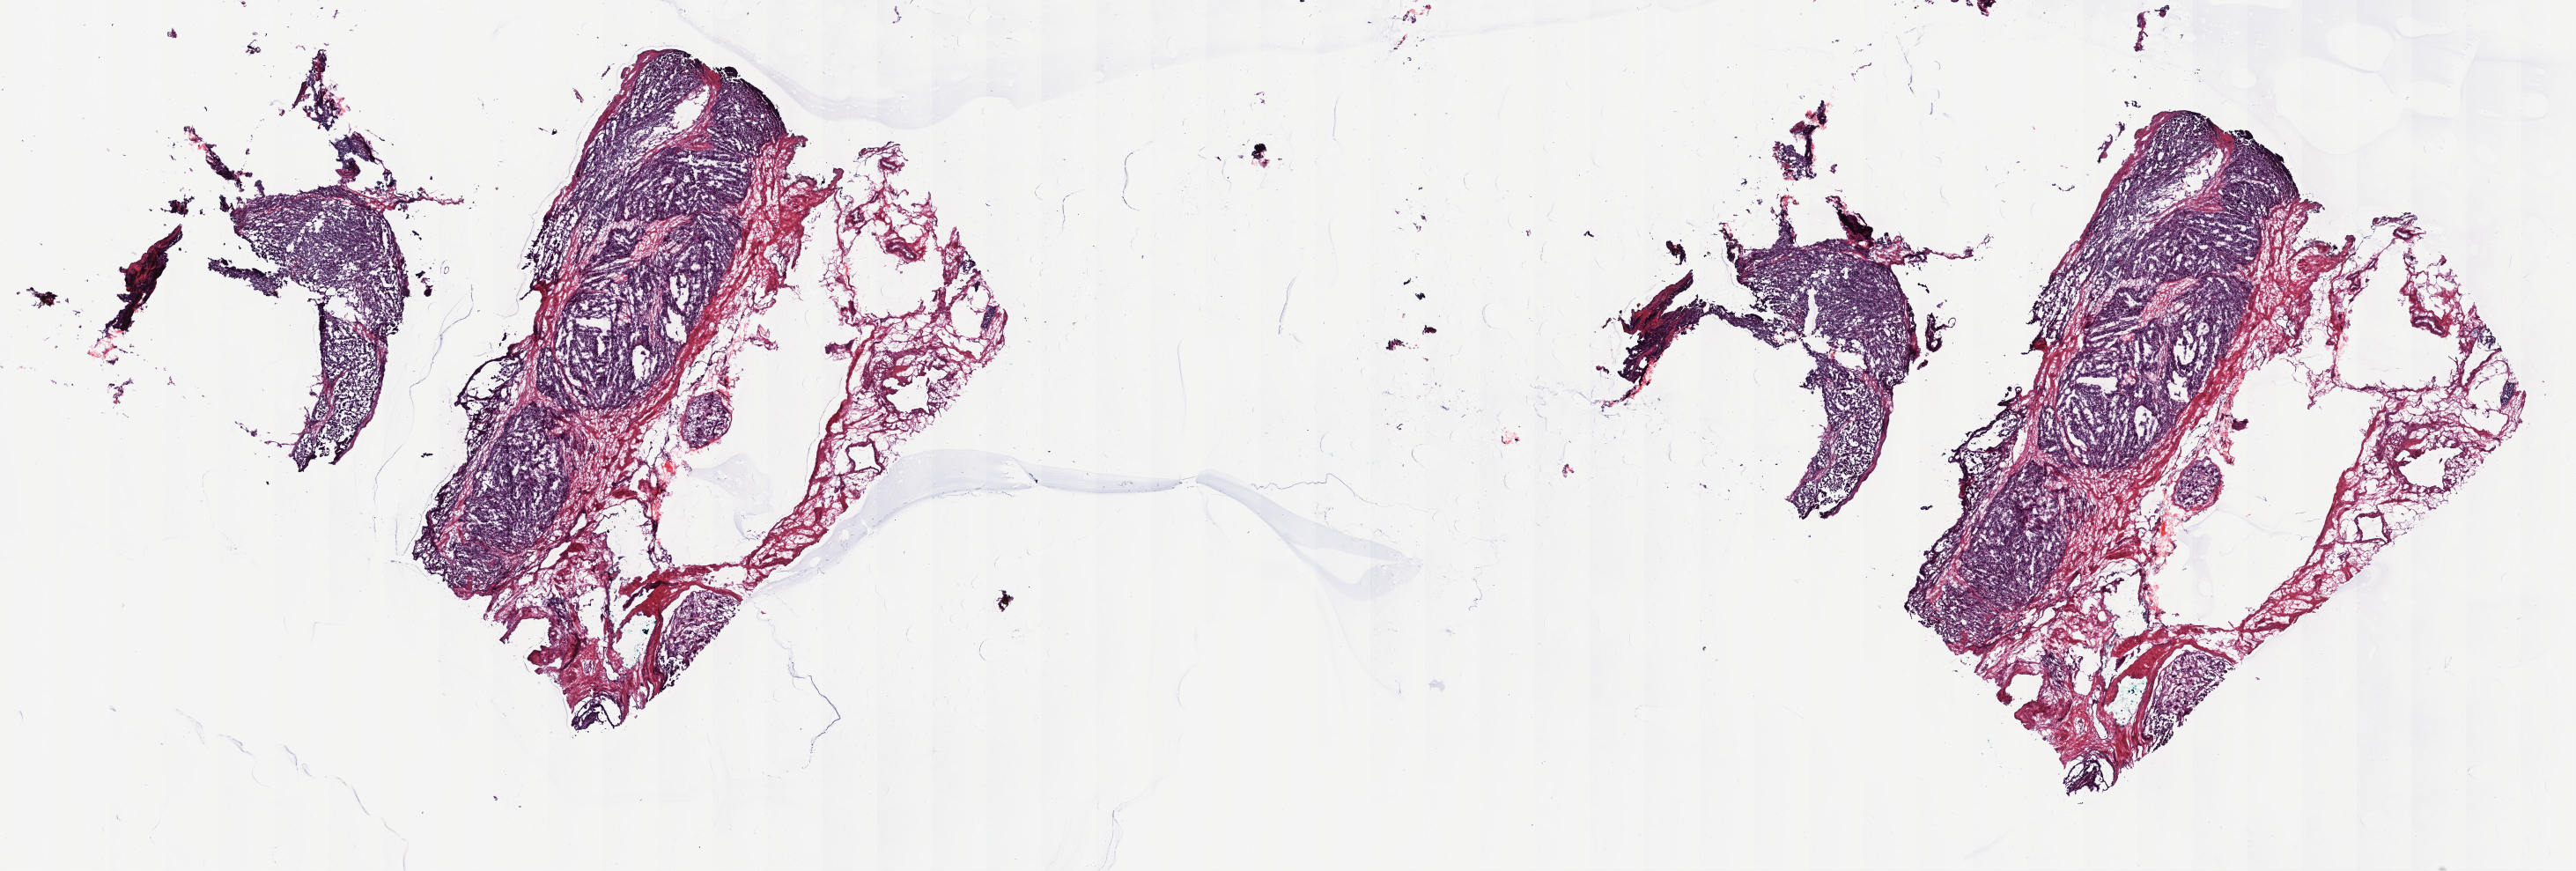
H&E-stained whole-slide image — shown as a low-resolution overview of the whole scanned area (about 23.7 x 8.0 mm, from a 40x scan), frozen section from the top of the tissue portion, primary tumour sample from the prostate. Patient: male, age at initial diagnosis 73 years. Gleason score: 9 (5+4). Pathologist review of this section (percent, as recorded): tumour cells 70%, tumour nuclei 80%, normal cells 10%, stromal cells 20%, necrosis 0%. Inflammatory infiltration, as recorded: lymphocyte infiltration 0%, monocyte infiltration 0%, neutrophil infiltration 0%.
* lymph nodes positive (case pathology): 2 of 16 examined
* pathologic diagnosis: Adenocarcinoma, NOS (prostate gland)